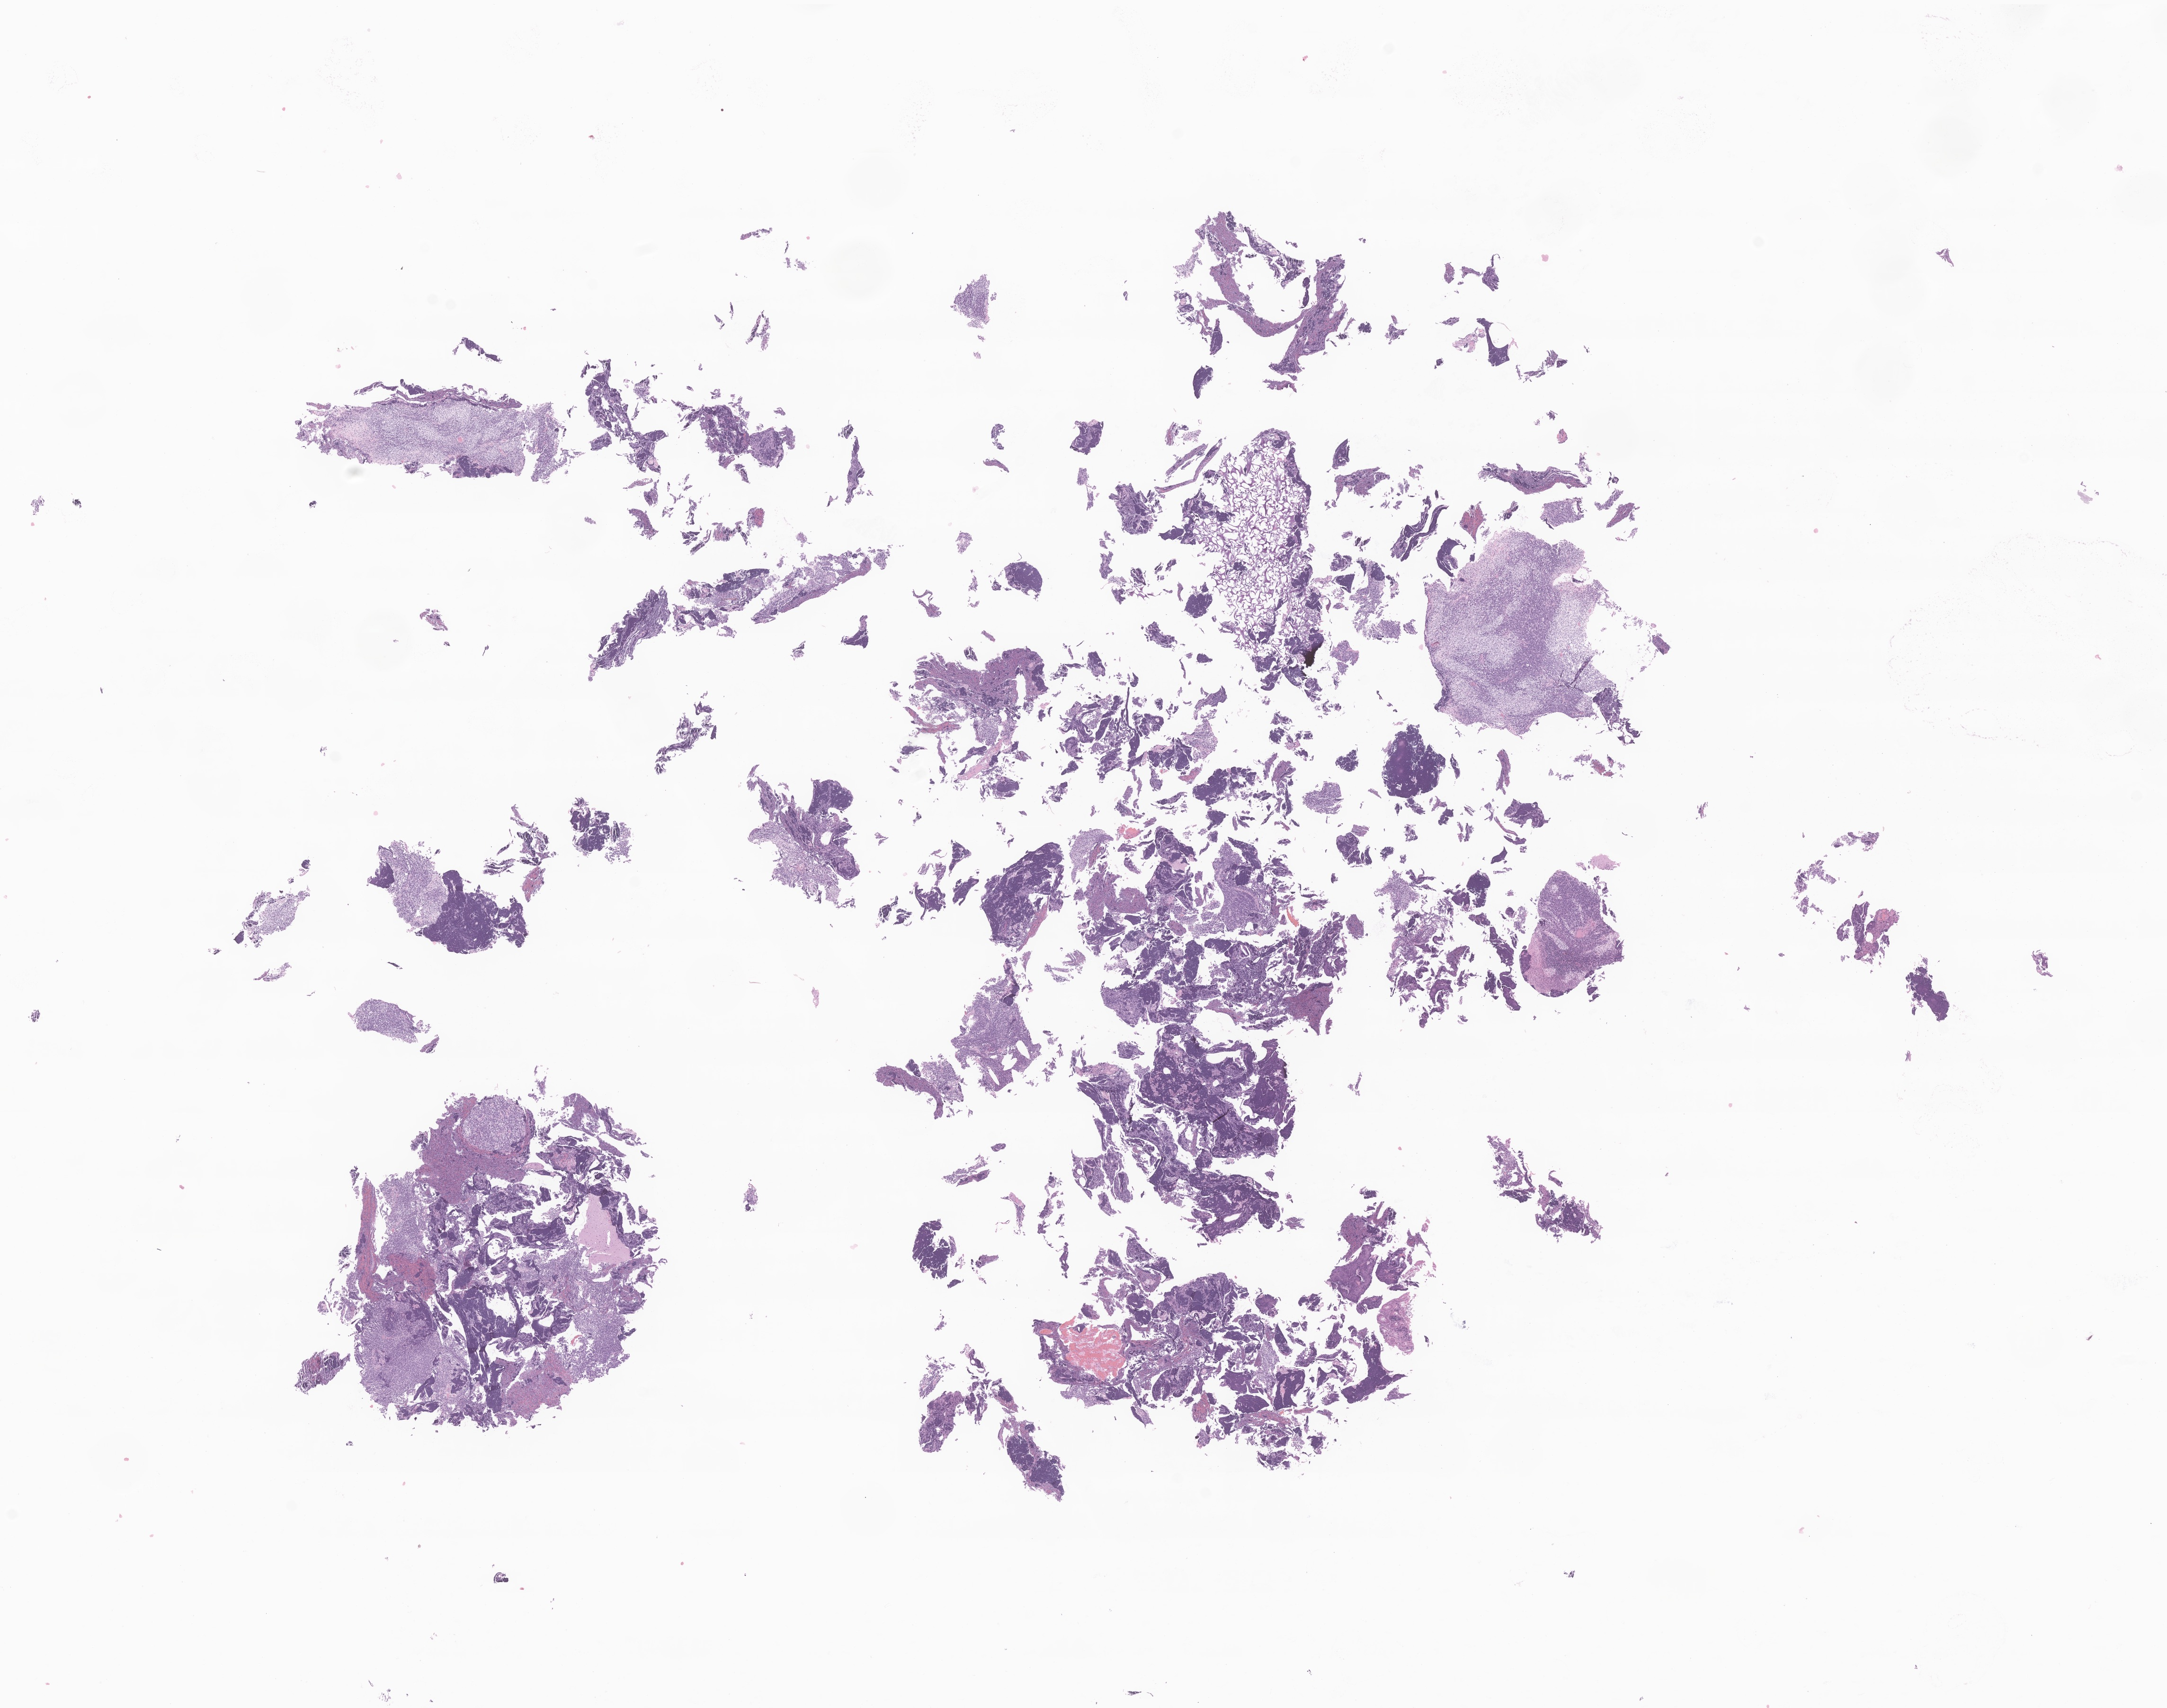
Hematoxylin and eosin (H&E) whole-slide image of tumor tissue from the brain — shown as a low-resolution overview of the whole scanned area (about 19.3 x 15.2 mm), formalin-fixed, paraffin-embedded (FFPE) tissue. Patient: male, age 70 months (5 years 10 months).
* diagnosis: Medulloblastoma, NOS